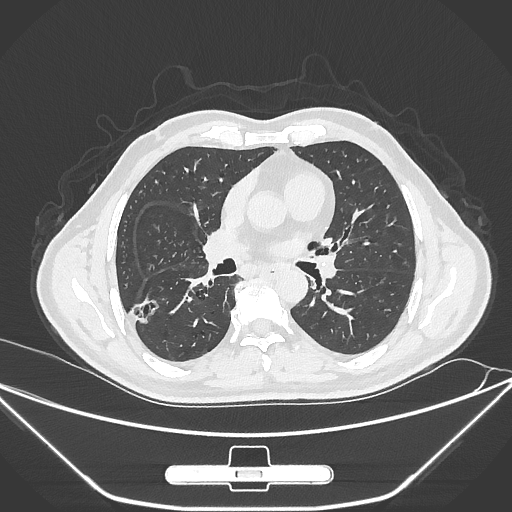
Chest CT, one axial slice; slice 153 of 310 in the series (ordered by position); reconstruction kernel IMR1,SharpPlus; 120 kVp; lung window (W 1500 / L -600 HU); 1 mm slice thickness; 512 × 512 image matrix, field of view 398 × 398 mm. Patient: male, 71 years. Case-level facts recorded for this patient, not image findings: clinical TNM (as recorded): T1c N0 M0.
Outlined on this slice (rectangle marked by the reading radiologist):
- lung tumour (recorded histology: adenocarcinoma): bounding box <128,292,171,335> (left, top, right, bottom; pixels)